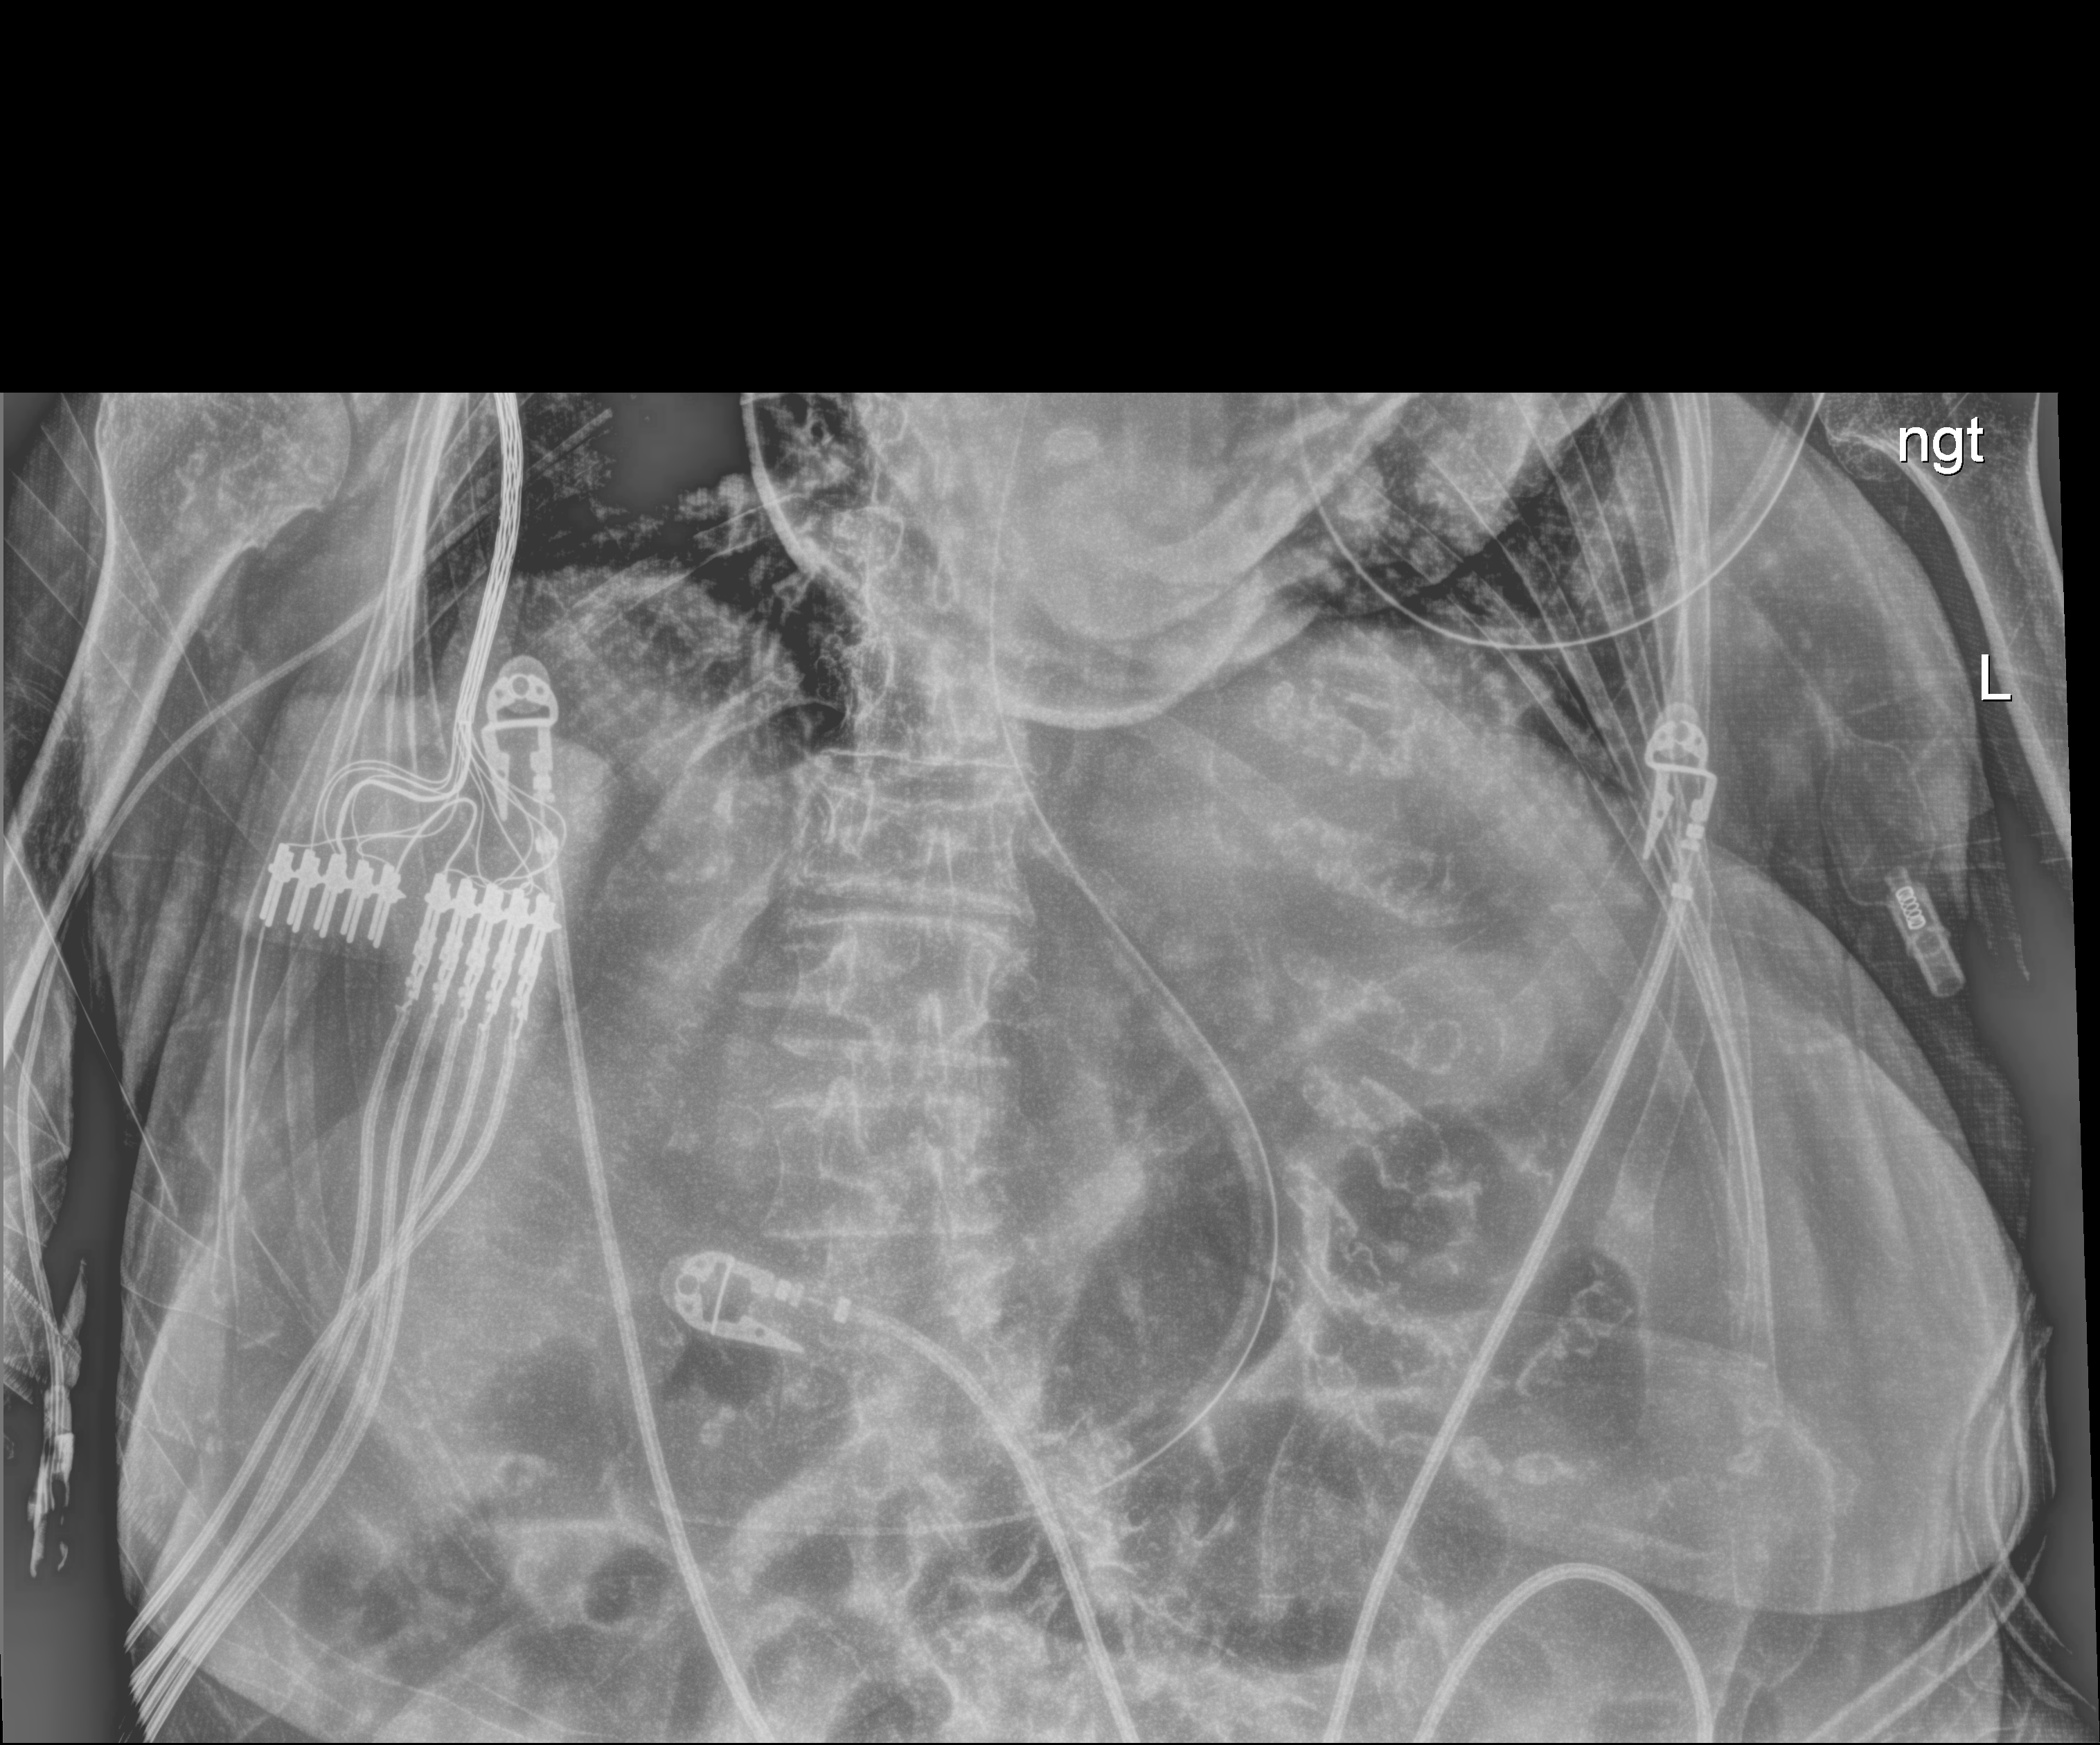
Bedside abdomen radiograph (digital radiography), anteroposterior (AP) projection. Female patient hospitalised with COVID-19, age 75–90 years.
Admission-level facts for this patient (not findings on this image; timing relative to this image not recorded):
- COPD (admission record): no